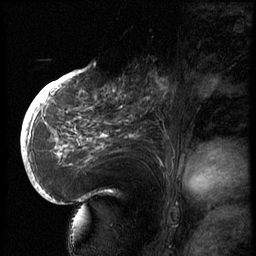
Breast MRI (dynamic contrast-enhanced), one sagittal slice. Slice 33 of 66 in the series (ordered by position). 3 images stored at this slice position (order not interpretable as contrast timing). 1.5 T. TE 4.2 ms, TR 8.9 ms. 256 × 256 image matrix. Patient: female, 56 years. From the clinical record (not read from this slice): setting: breast cancer imaged before/during neoadjuvant chemotherapy.
Annotated regions visible in this slice (semi-automatic segmentation, software-assisted and operator-edited):
- analysis volume of interest (the breast-tissue region the enhancement analysis was run in; not a lesion): bounding box [x1, y1, x2, y2] px = [129, 62, 194, 127]
- tumour enhancement mask (voxels above the 140 % enhancement threshold inside the analysis volume of interest): [149, 72, 171, 99]